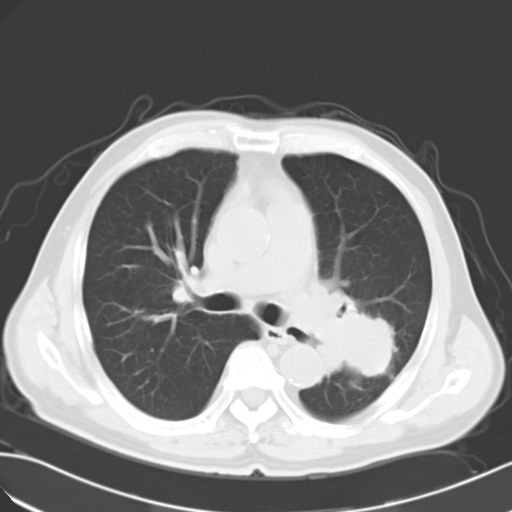
Chest CT, one axial slice; position 17 of 28 along the scan axis; reconstruction kernel B40f; lung window (W 1500 / L -600 HU); 10 mm slice thickness; 512 × 512 image matrix, field of view 353 × 353 mm. Patient: male, 63 years. Case-level facts recorded for this patient, not image findings: clinical TNM (as recorded): T3 N3 M1a.
Structures marked on this image (rectangle marked by the reading radiologist):
- lung tumour (recorded histology: large cell carcinoma): bounding box [x1, y1, x2, y2] px = [279, 265, 390, 387]